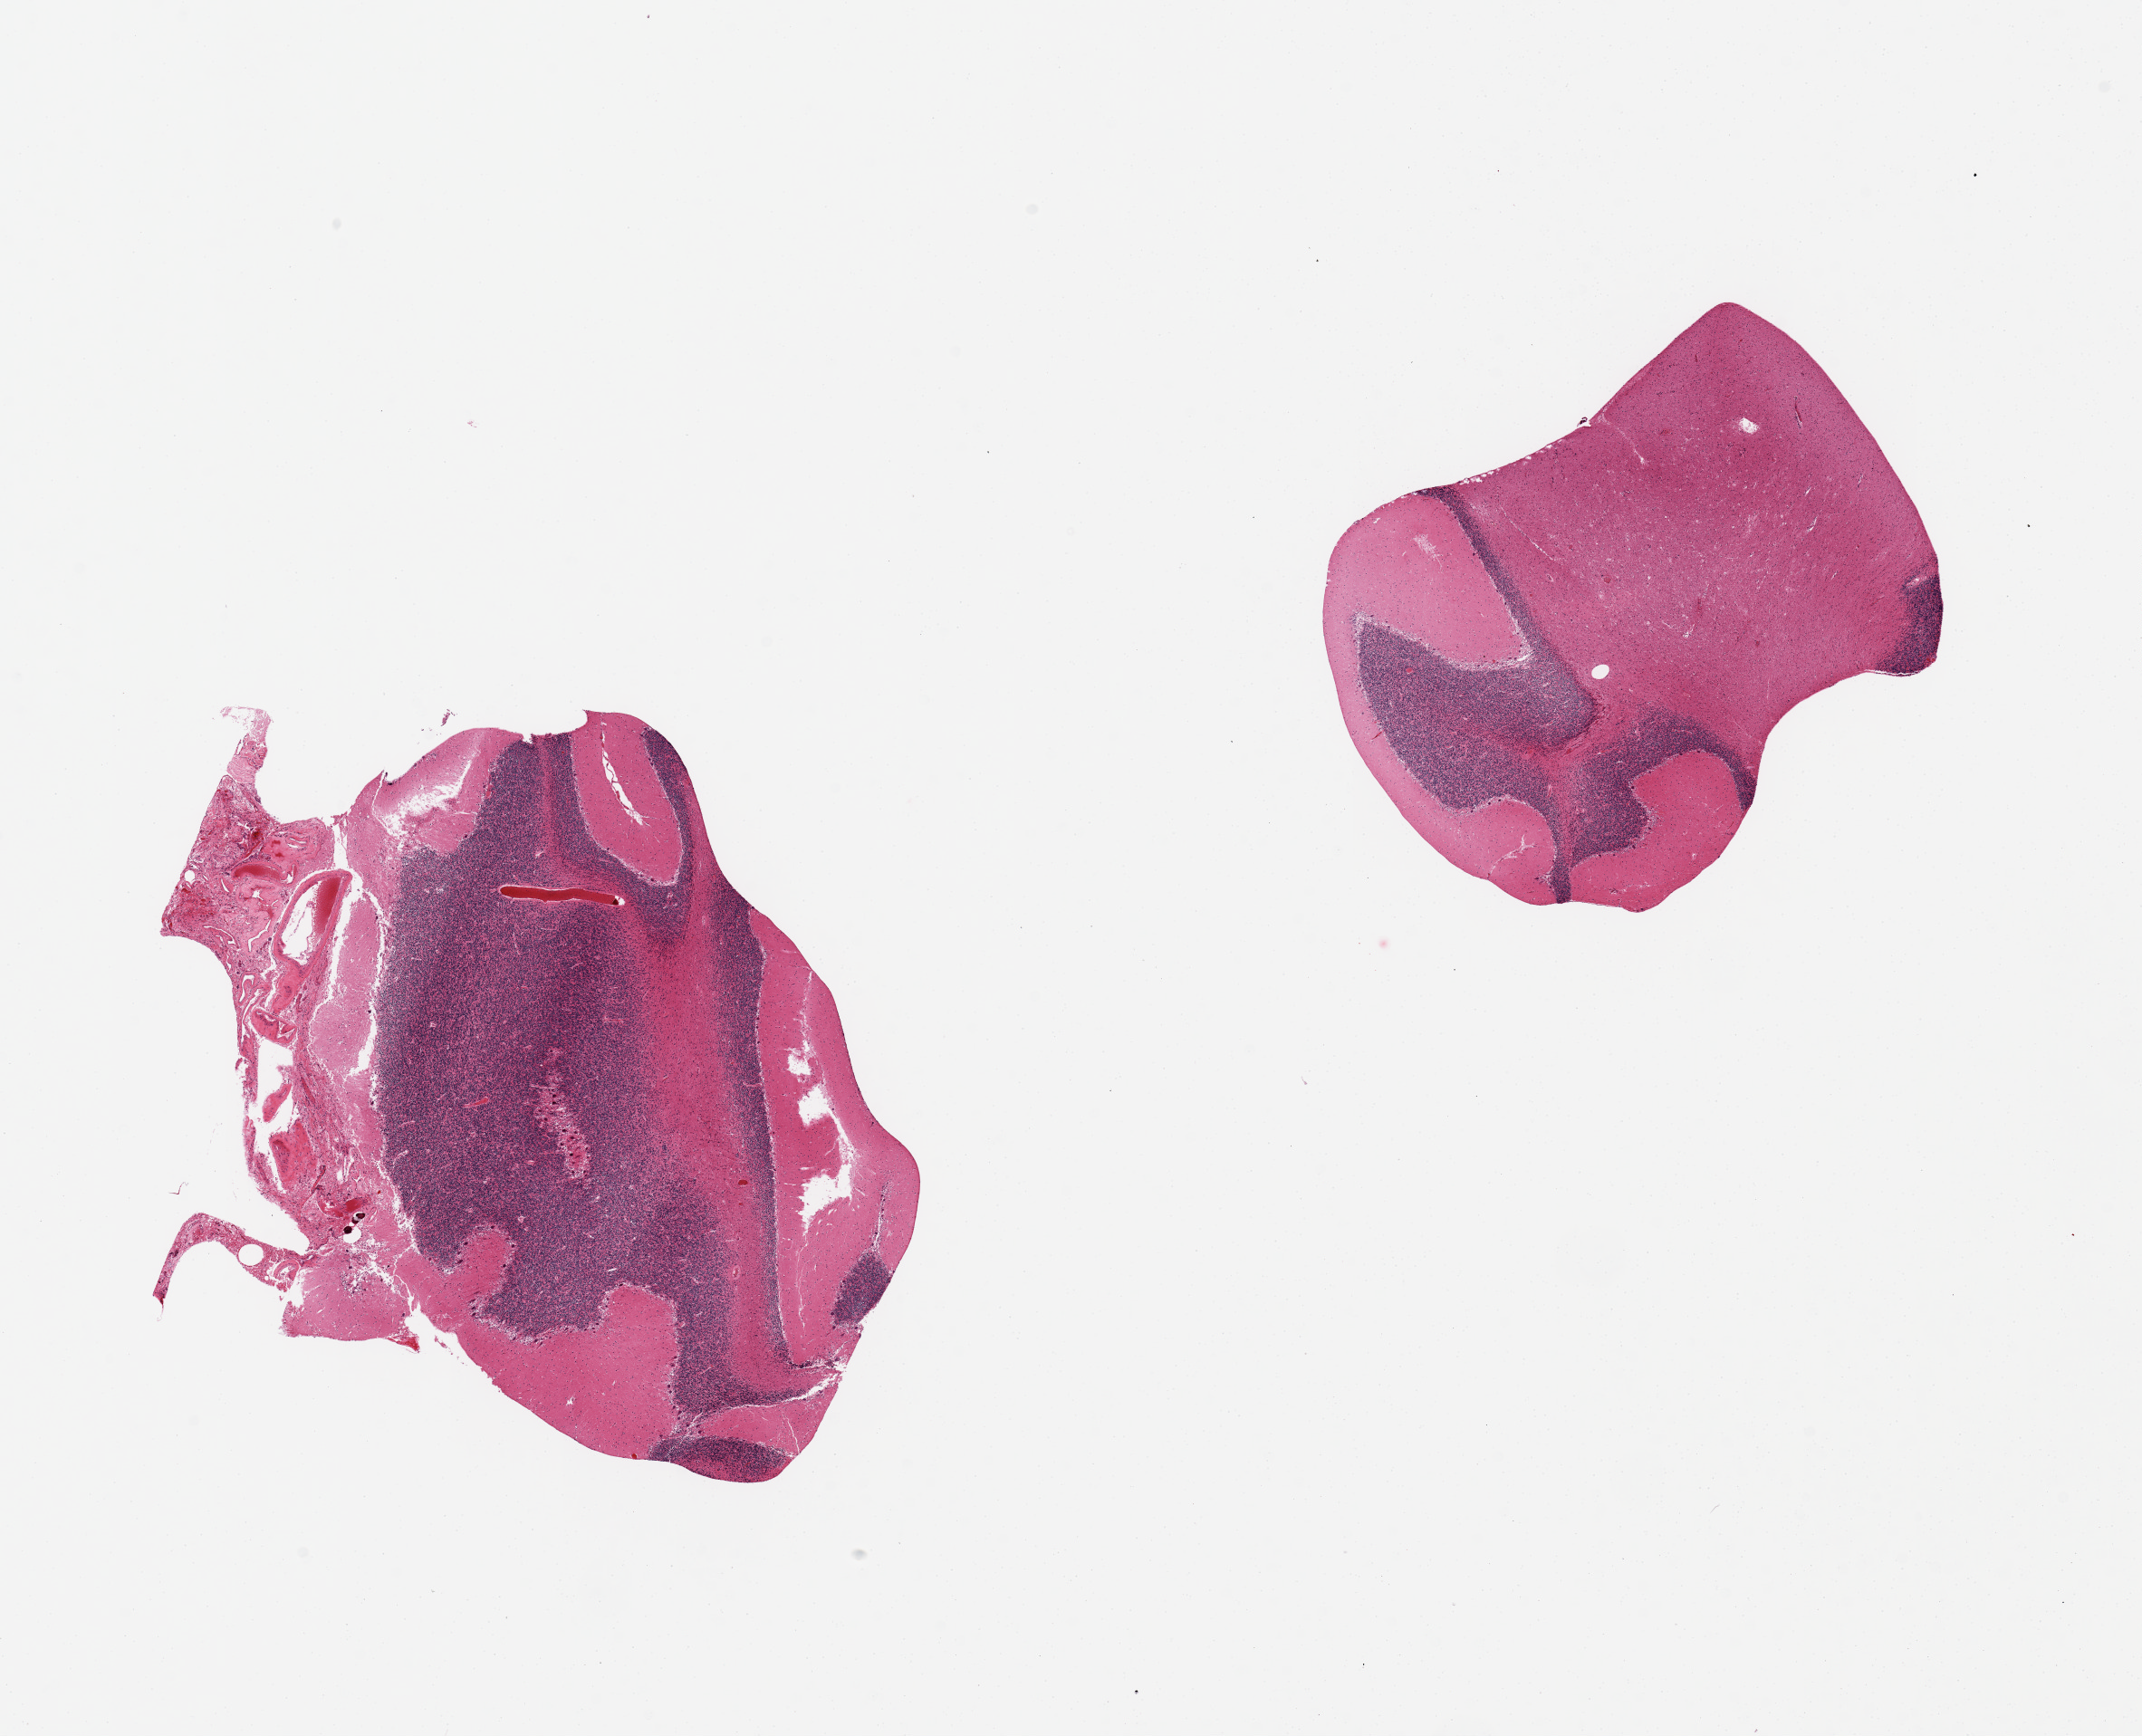
Digitized H&E-stained section, brightfield, whole scanned area (about 18.7 x 15.2 mm, acquisition: 20x scan) shown as a low-resolution overview. PAXgene-fixed, paraffin-embedded tissue. Section of cerebellum (target tissue). Tissue donor sample.
* reviewer comment on this tissue sample: 2 pieces, attached portion of meninges